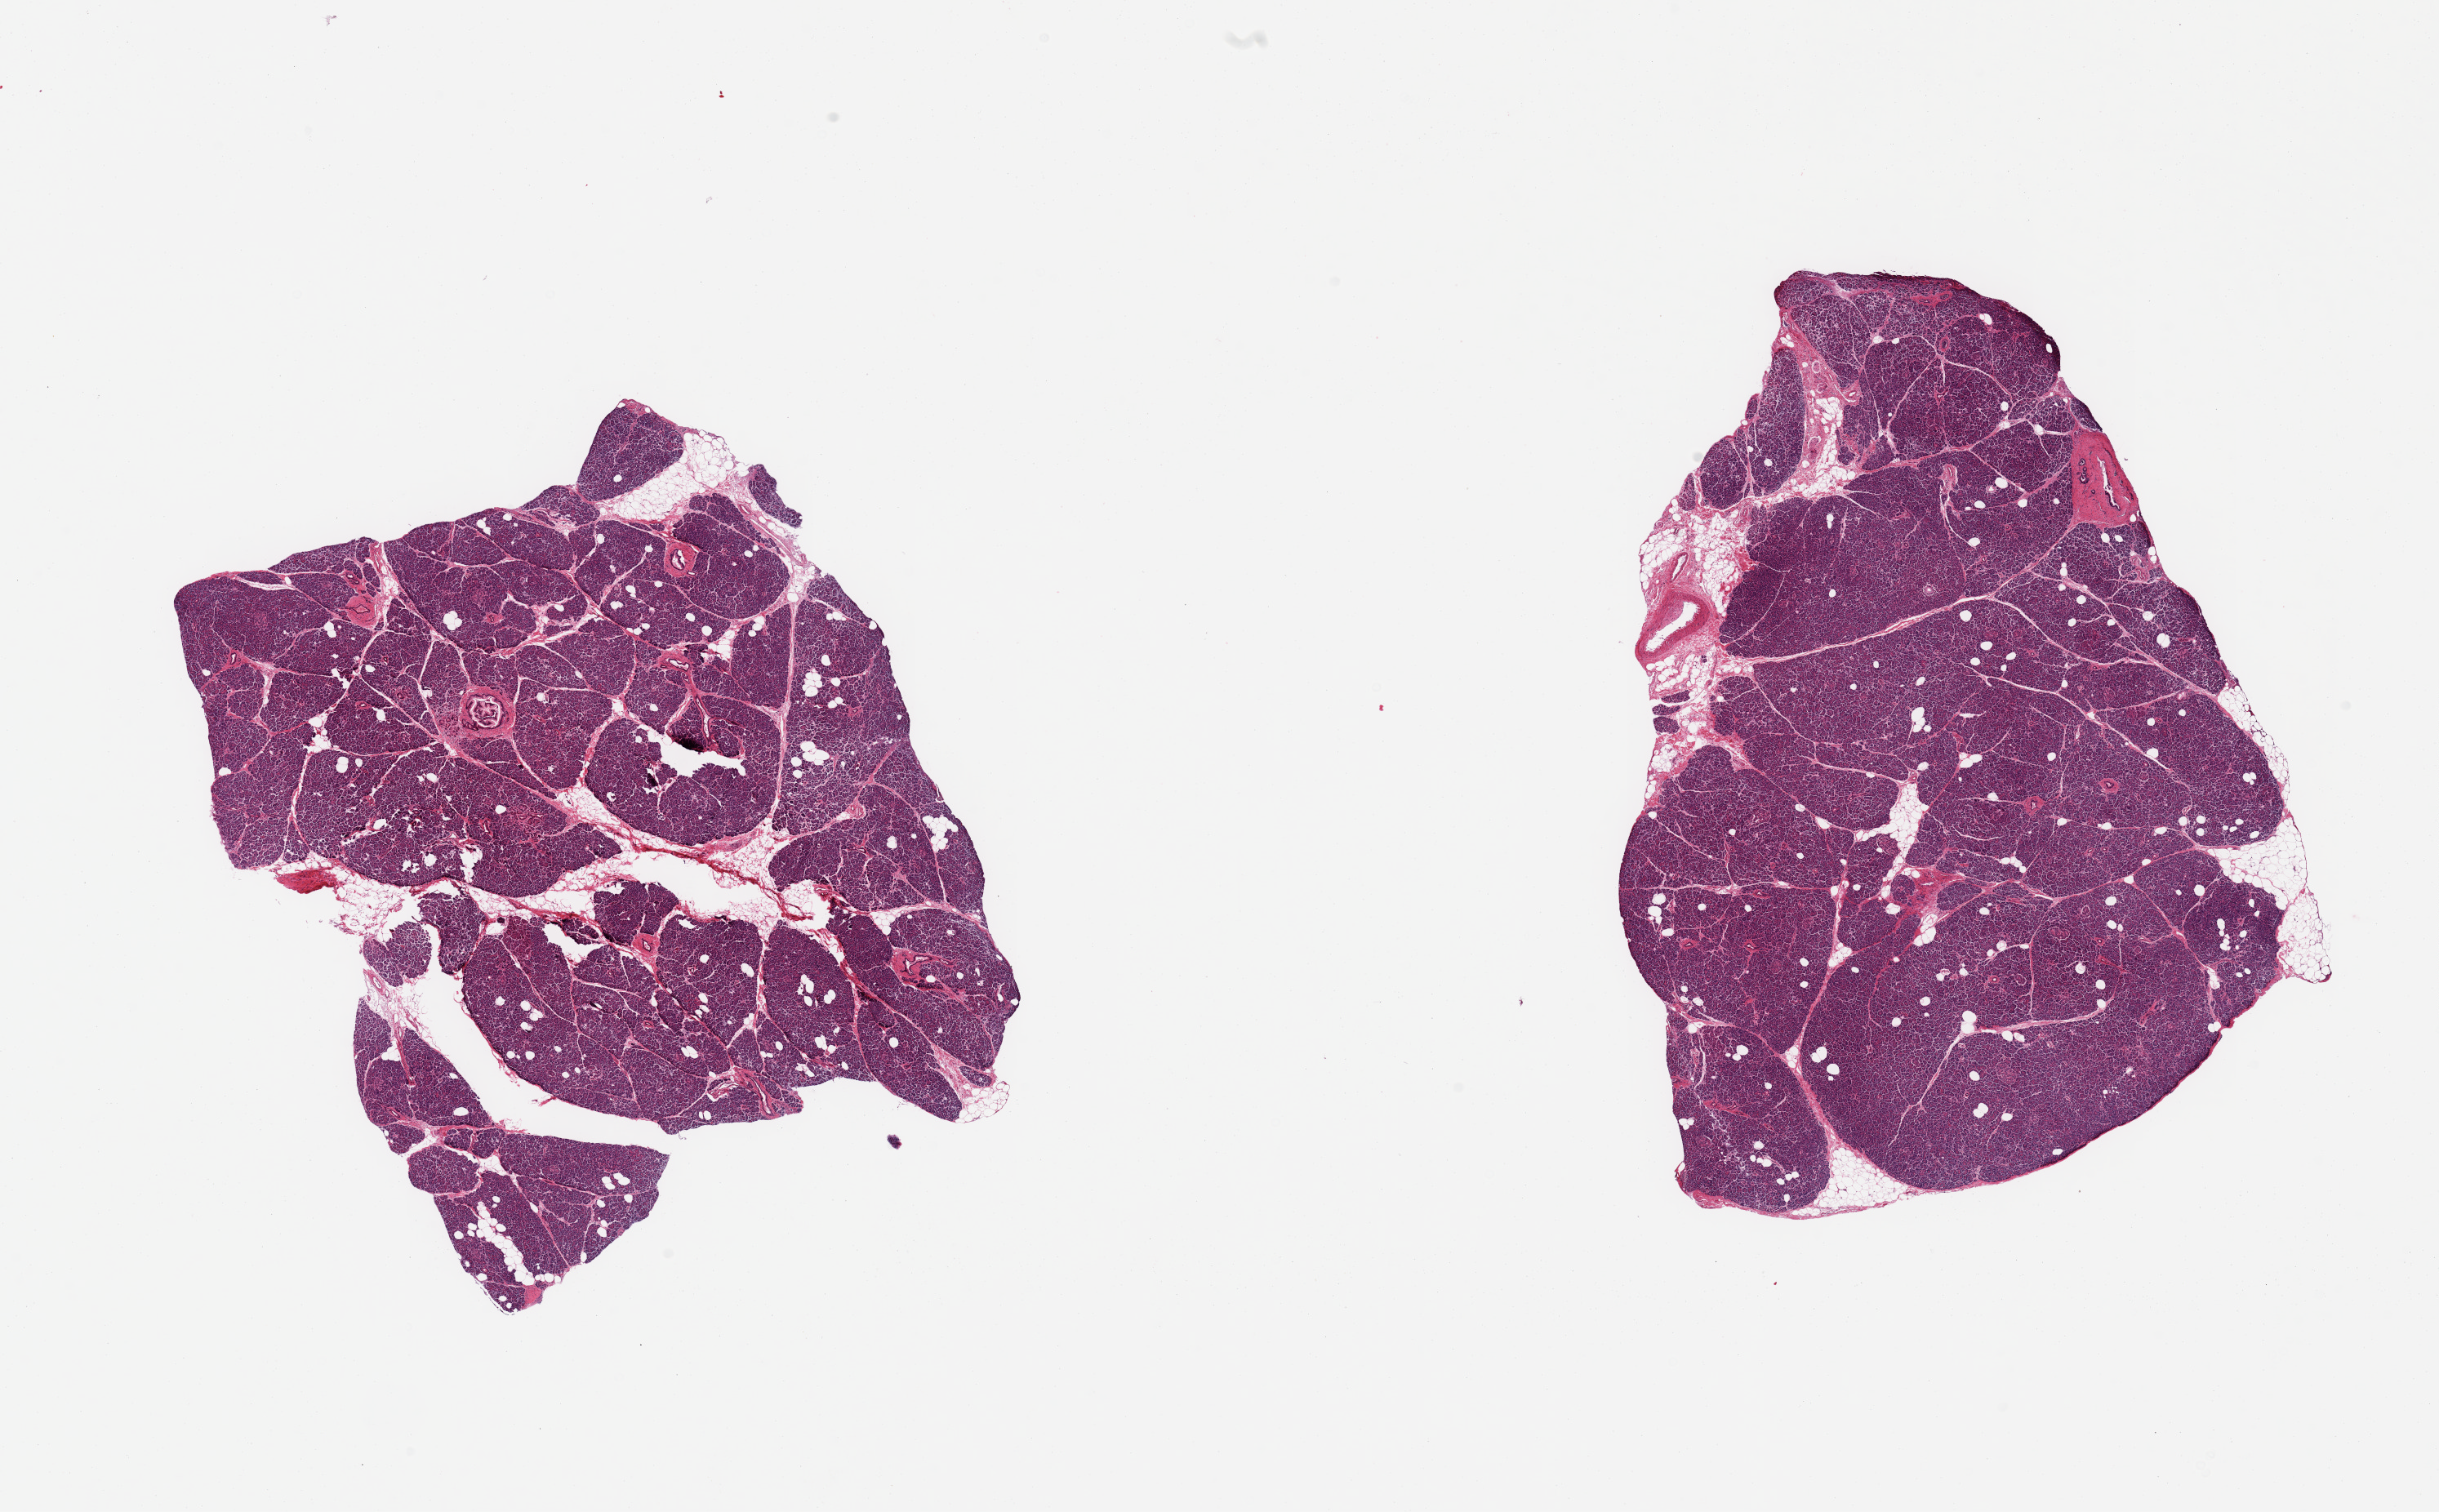
Whole-slide image, haematoxylin and eosin stain, shown as a low-resolution overview of the whole scanned area (about 23.6 x 14.6 mm); PAXgene-fixed, paraffin-embedded tissue; section of pancreas (target tissue); tissue donor sample. Female donor.
• review note (as recorded): 2 pieces; 10% internal fat